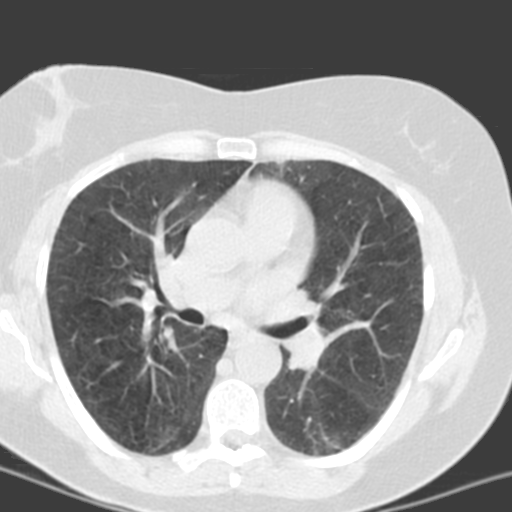
Chest CT (low-dose screening protocol), one axial image; third screening round (two years after baseline); lung window (W 1500 / L -600 HU); standard (soft-tissue) reconstruction kernel (B); 512 × 512 image matrix, field of view 290 × 290 mm. Female participant, aged 55 years at enrolment. Current smoker at enrolment.
• Expert-annotated lung lesion, bounding box <289,413,367,465> (left, top, right, bottom; pixels).
• The screening reader recorded 6 non-calcified nodules or masses ≥4 mm on this exam (left lower lobe, left lower lobe, left upper lobe, lingula, lingula, right middle lobe); which of them this box marks is not recorded.
• Official screen result: positive, no significant change: stable abnormalities potentially related to lung cancer, unchanged since the prior screening exam.